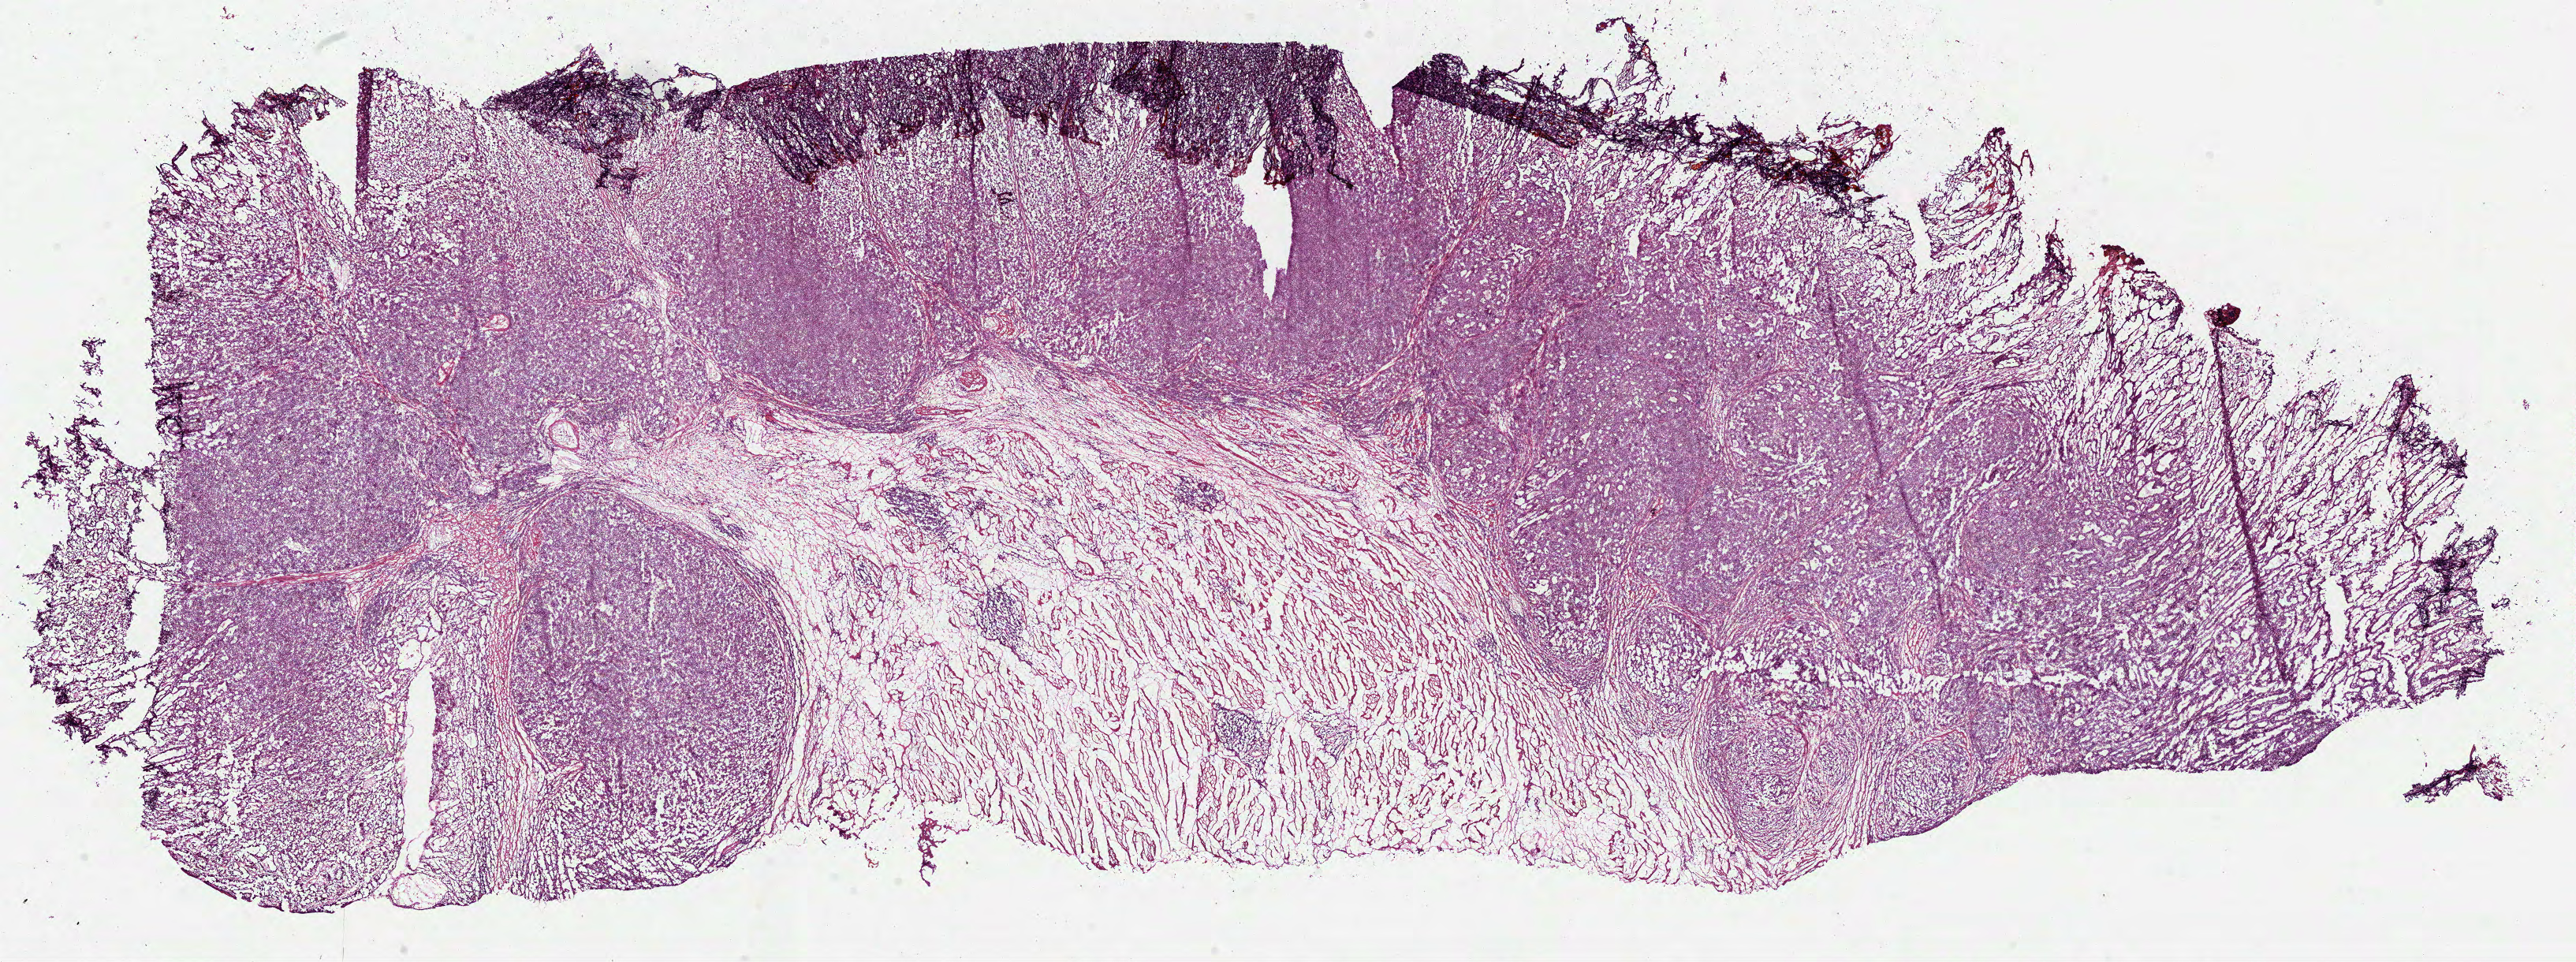
Hematoxylin and eosin (H&E) stained whole-slide image, shown as a low-resolution overview of the whole scanned area (about 26.3 x 9.8 mm, slide scanned at 40x); frozen section from the bottom of the tissue portion; sample: primary tumour, stomach. Patient: male, age at initial diagnosis 56 years. Histologic grade: G3 (poorly differentiated). Slide review estimates, as recorded: tumour cells 68%, tumour nuclei 75%, normal cells 12%, stromal cells 20%, necrosis 0%.
- lymph nodes positive (case pathology): 1 of 8 examined
- AJCC pathologic stage: IIIB (7th edition)
- pathologic diagnosis: Adenocarcinoma, NOS